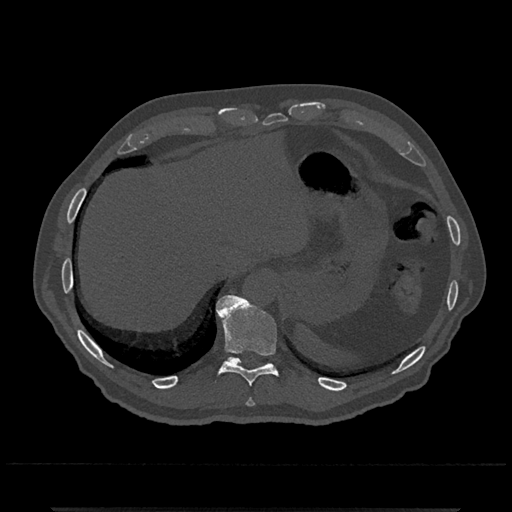
CT including the spine, one axial slice; slice 547 of 797 in the series (ordered by position); reconstruction kernel Br40s/3; bone window (W 1800 / L 400 HU); 0.5 mm slice thickness; 512 × 512 image matrix, field of view 393 × 393 mm. Male patient, age 67 years. Case-level facts recorded for this patient, not image findings: primary cancer: prostate.
Annotated regions visible in this slice (semi-automatic segmentation, software-assisted and operator-edited):
- T10 vertebra: box from (x=209, y=295) to (x=278, y=386) px
- T11 vertebra: (x=227, y=357)–(x=267, y=366)
- T9 vertebra: (x=246, y=400)–(x=255, y=407)